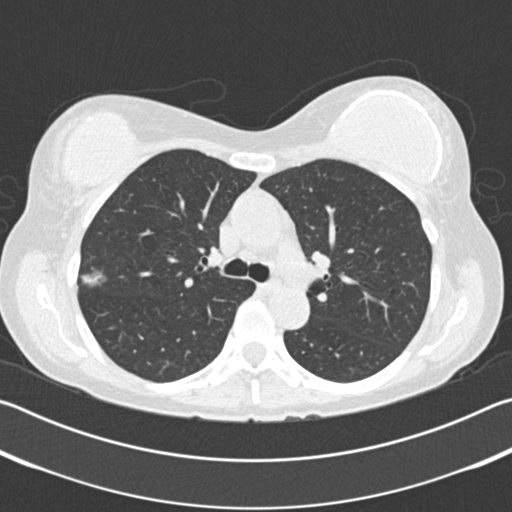
Axial slice from a low-dose chest CT screening exam, second annual screen, lung window (W 1500 / L -600 HU), standard (soft-tissue) reconstruction kernel (B30f), slice 61 of 183 in the series. Female participant, aged 58 years at enrolment. Former smoker at enrolment.
Expert reader's lesion annotation, bounding box <64,257,119,304> (left, top, right, bottom; pixels). Reader record for this screening exam (exam-level; its link to the box is not recorded): non-calcified nodule or mass ≥4 mm, right upper lobe, 15 × 13 mm, poorly defined margins, ground glass attenuation, pre-existing on the prior screen: no. Later outcome: lung cancer diagnosed 120 days after this screen — bronchiolo-alveolar adenocarcinoma, NOS, right upper lobe, well differentiated (G1), stage IA (AJCC 6th edition).